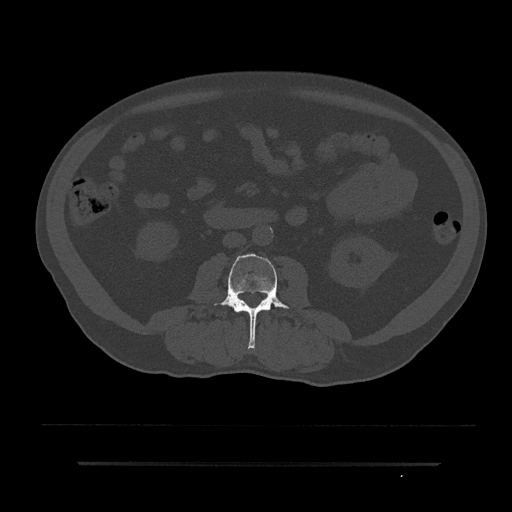
CT including the spine, one axial slice; reconstruction kernel Br40s/3; 120 kVp; bone window (W 1800 / L 400 HU); 0.5 mm slice thickness; 512 × 512 image matrix, field of view 464 × 464 mm. Male patient, age 59 years. From the clinical record (not read from this slice): primary cancer: bile ducts; vertebrae with lytic lesions (as recorded): T10.
Structures marked on this image (semi-automatically segmented with operator editing):
- L3 vertebra: box from (x=213, y=253) to (x=290, y=349) px